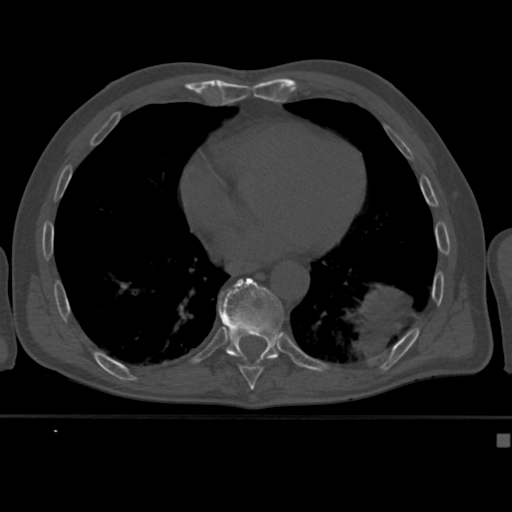
CT including the spine, one axial slice. Slice 238 of 430 in the series (ordered by position). Bone window (W 1800 / L 400 HU). 512 × 512 image matrix. Patient: male, 64 years. Case-level facts recorded for this patient, not image findings: primary cancer: uterus.
Outlined on this slice (semi-automatic segmentation, software-assisted and operator-edited):
- T10 vertebra: bounding box [x1, y1, x2, y2] px = [218, 278, 283, 366]
- T9 vertebra: [239, 365, 263, 382]